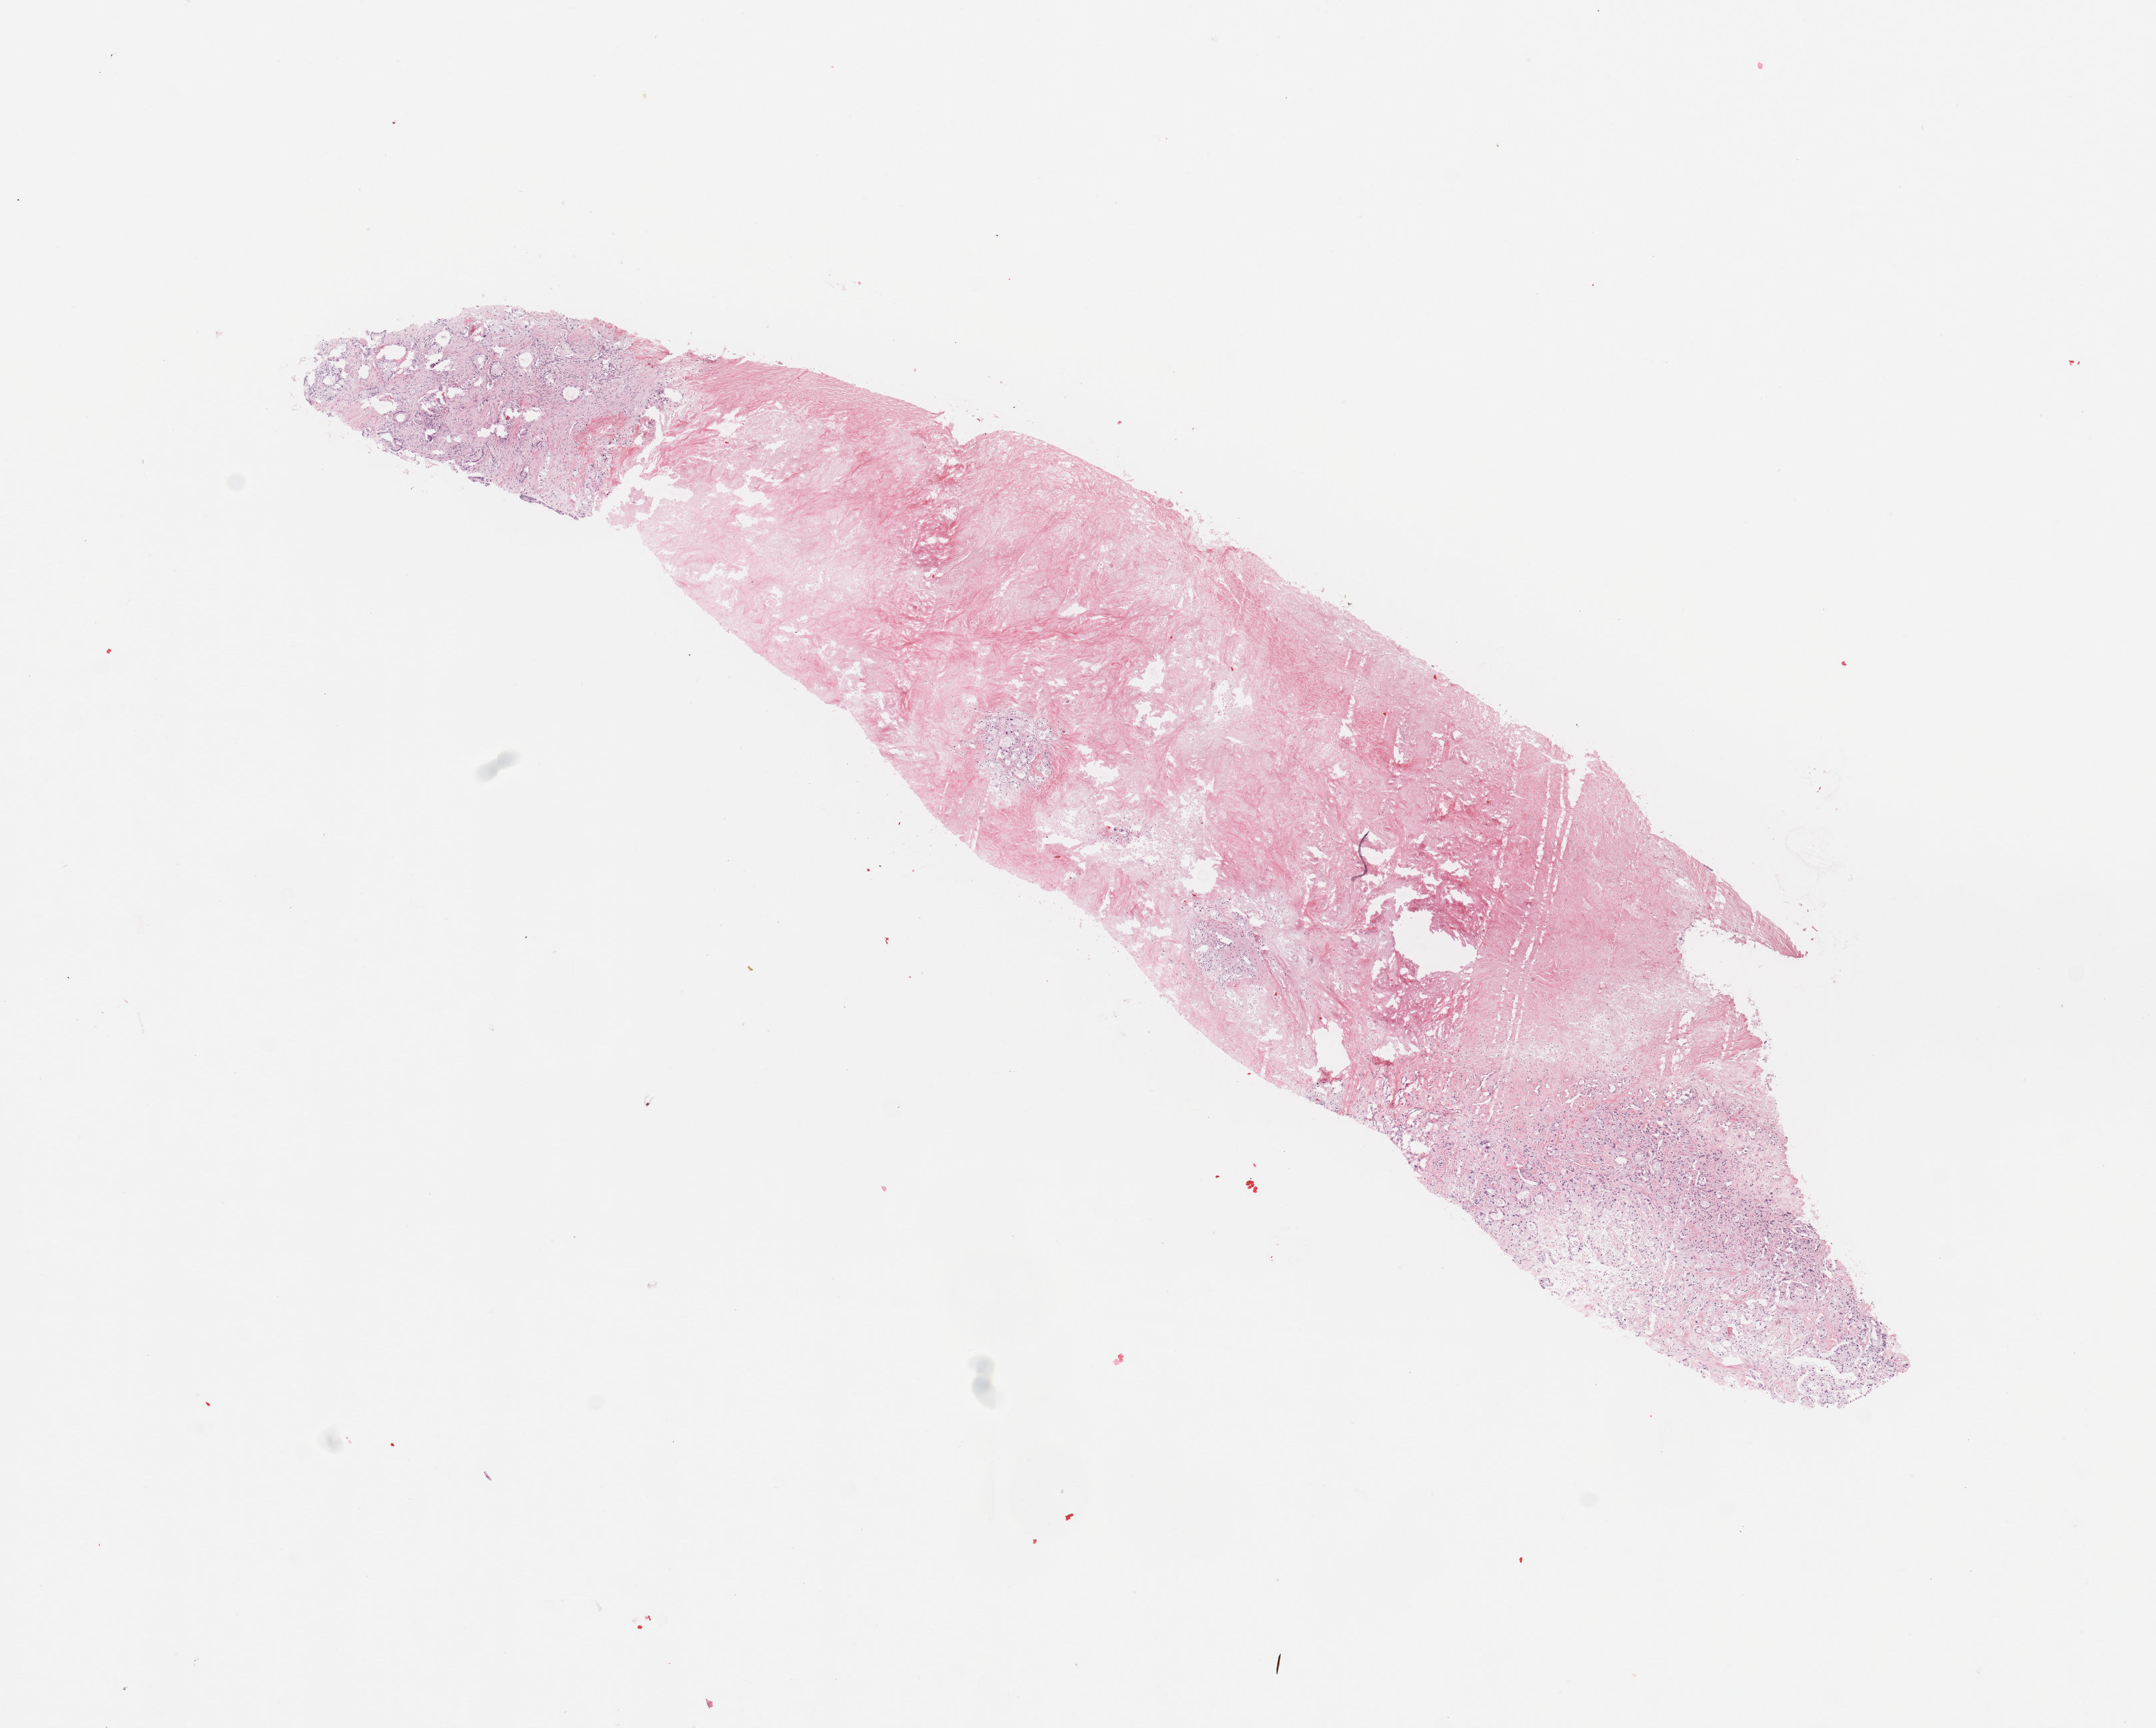
Digitized H&E tissue section (whole slide), low-resolution overview of the scanned area, about 12.8 x 10.3 mm; pancreas, tumour tissue. 54-year-old male patient. Histologic grade: G2 (moderately differentiated).
Primary tumour site (as recorded): tail. Diagnosis: Infiltrating duct carcinoma, NOS. AJCC pathologic stage: IIB.